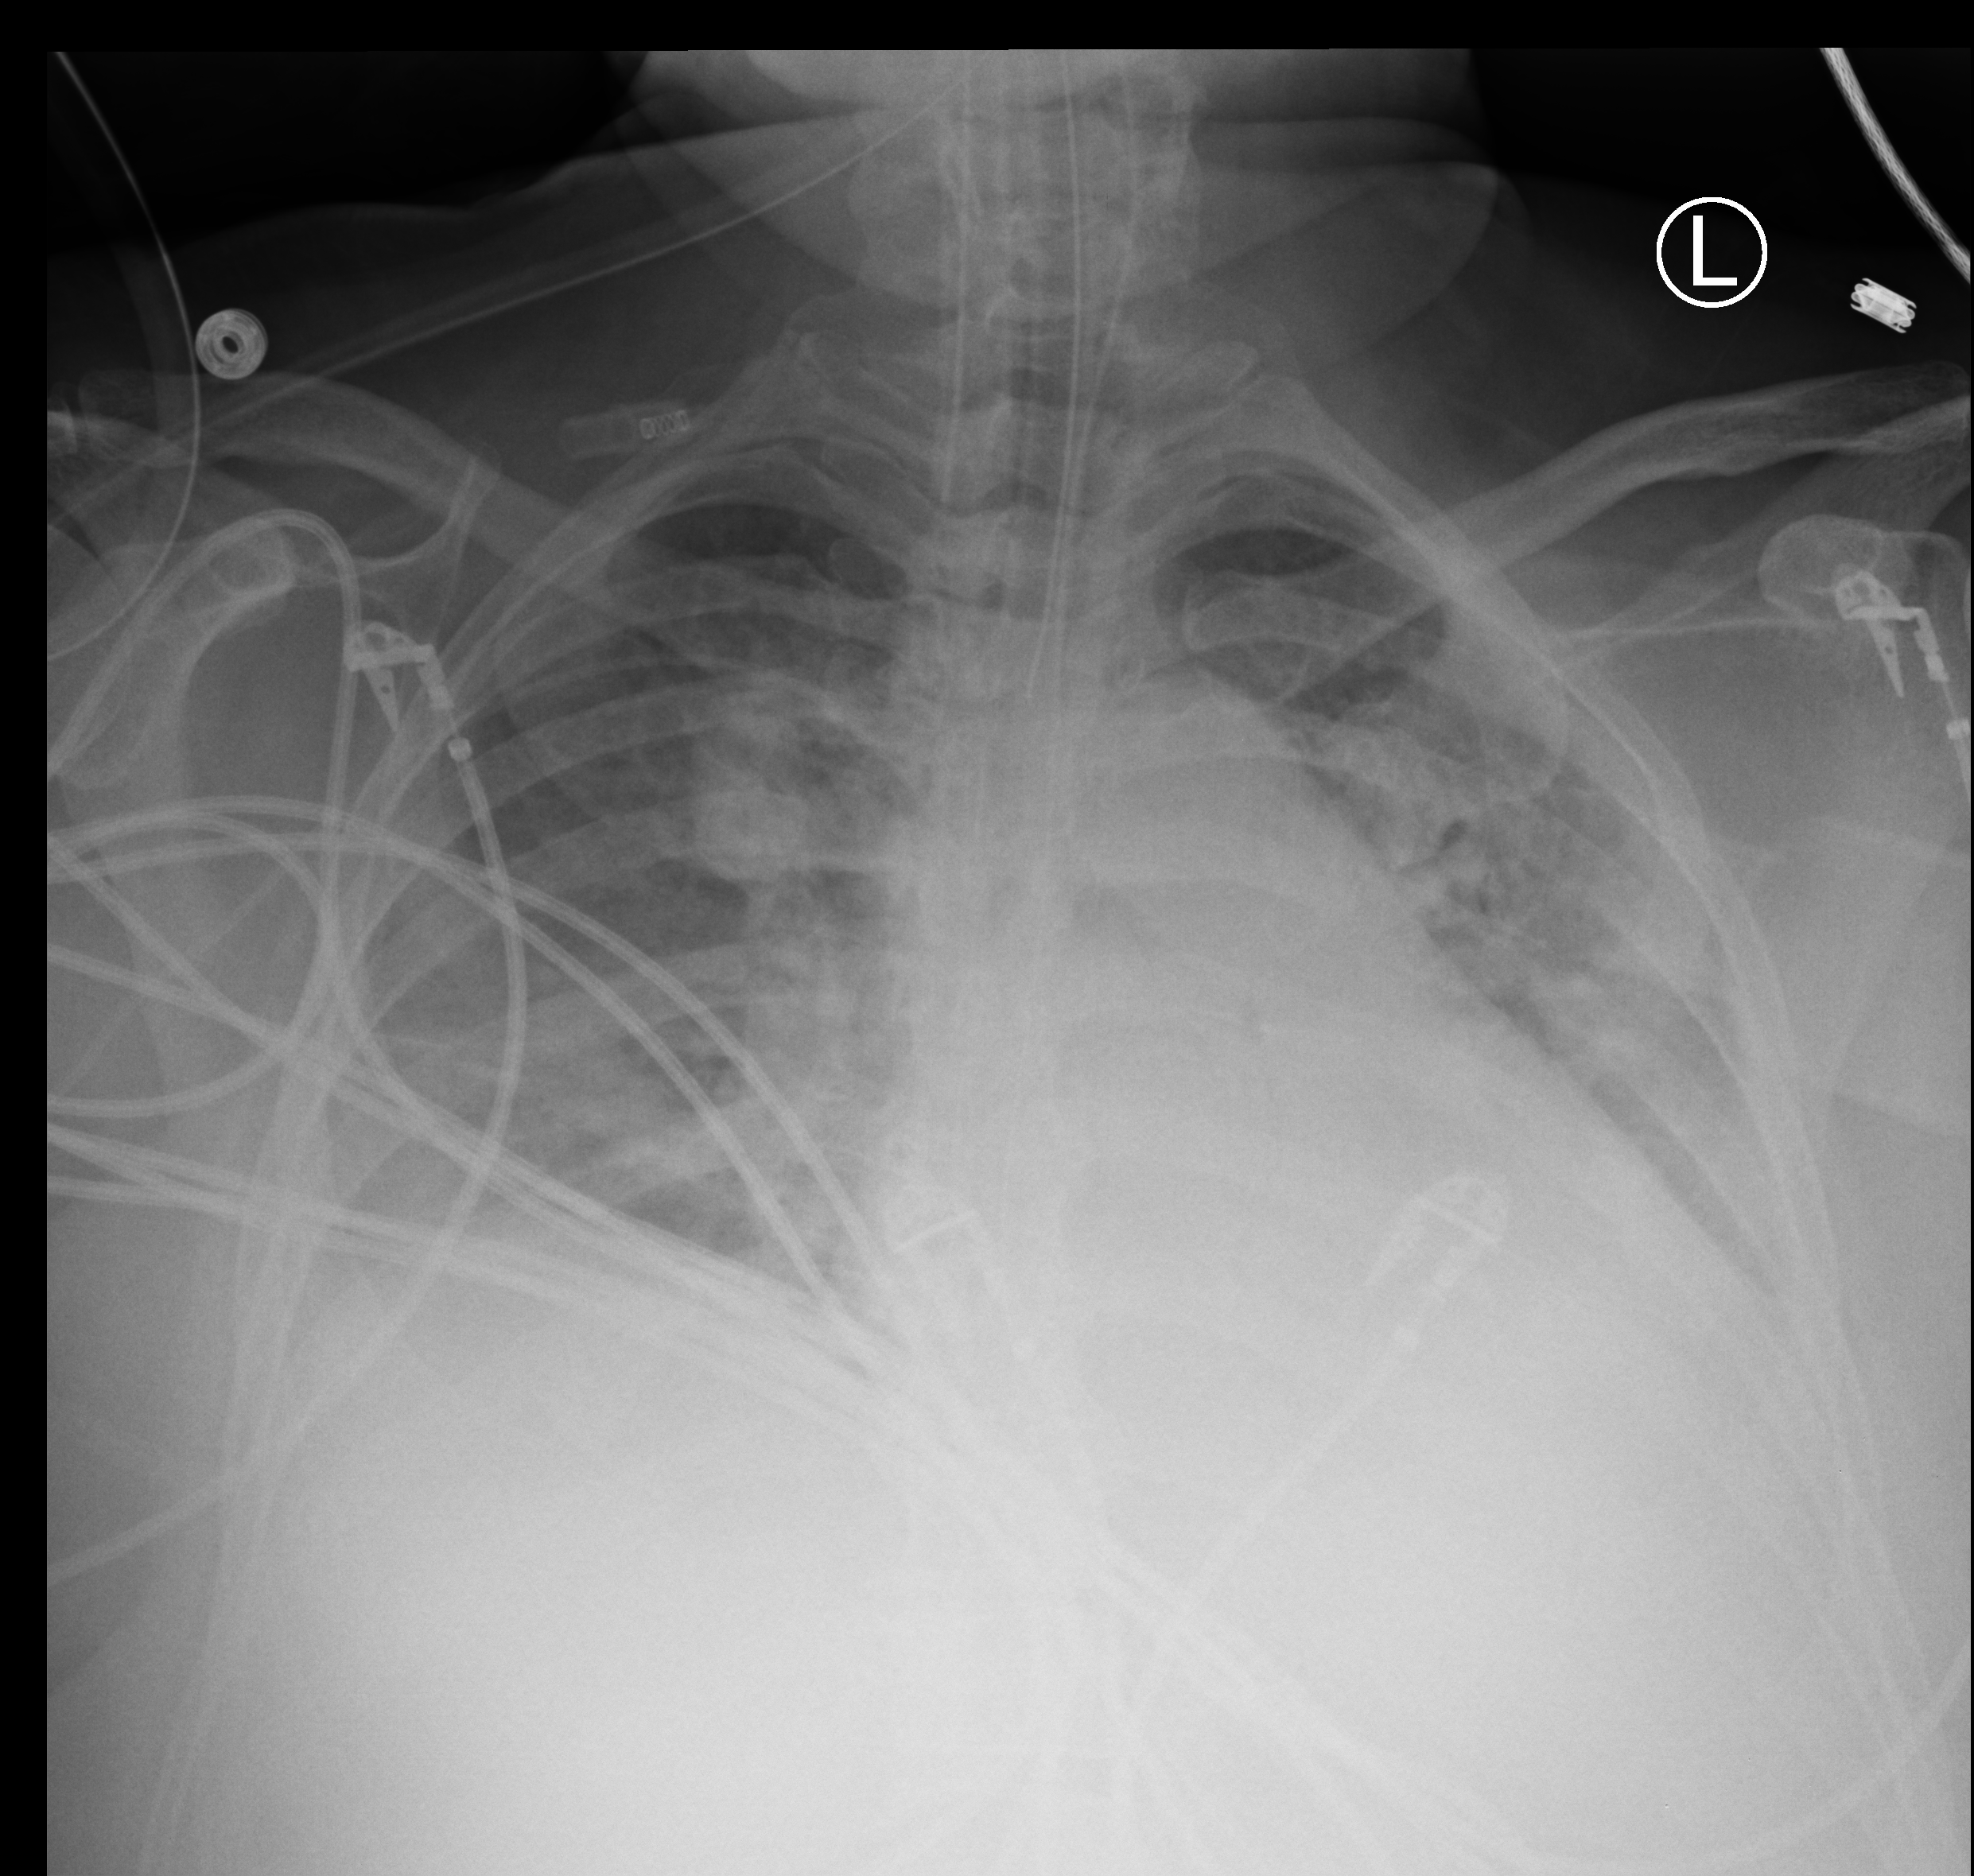
Portable chest radiograph; anteroposterior (AP) projection. Patient hospitalised with COVID-19; female, aged 60–74 years.
Admission-level facts for this patient (not findings on this image; timing relative to this image not recorded):
- admitted to intensive care during this hospital stay: yes